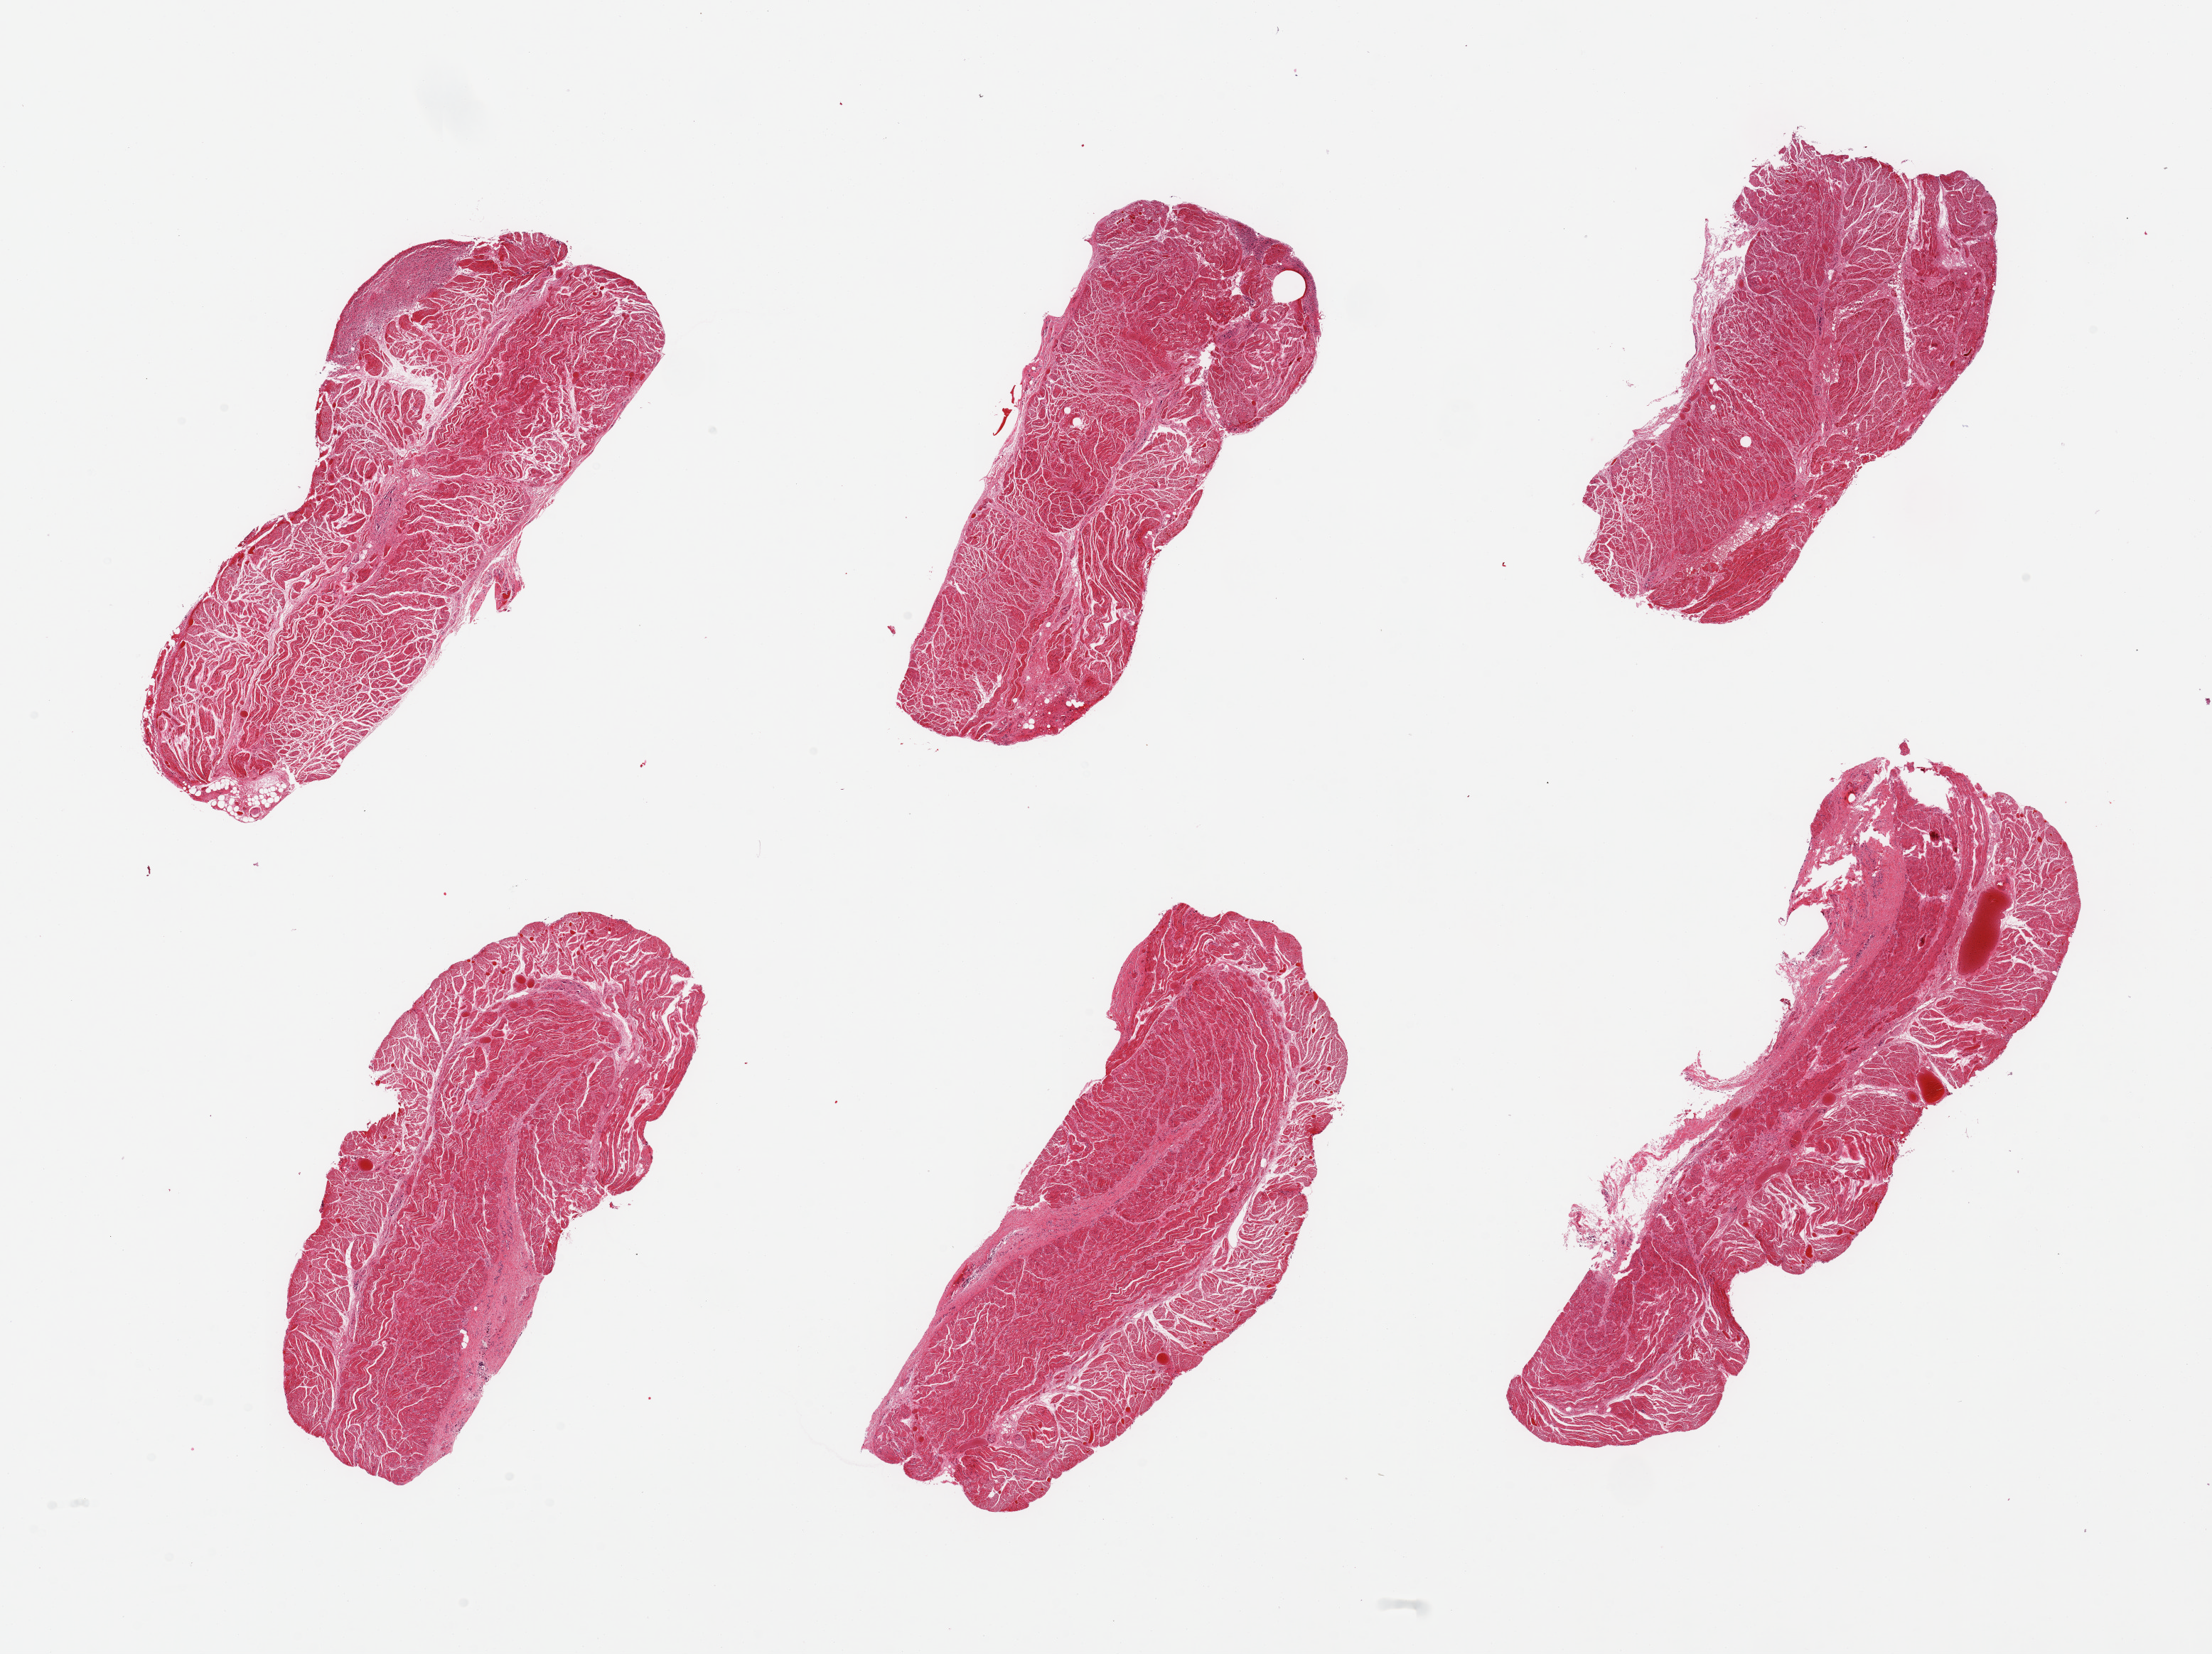
Whole-slide image, H&E stain — a low-resolution overview of the entire scanned area, about 24.6 x 18.4 mm. PAXgene-fixed, paraffin-embedded tissue. Target tissue: gastroesophageal junction. Tissue donor sample. Donor: male.
Reviewer comment on this tissue sample: 6 pieces, confirmed target muscularis.